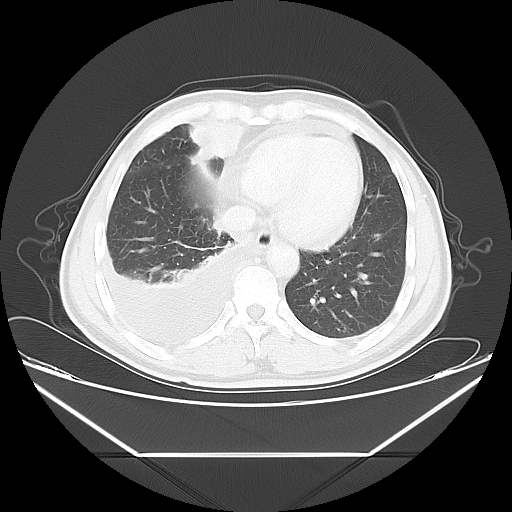
Chest CT, one axial slice; slice 15 of 56 in the series (ordered by position); reconstruction kernel LUNG; 120 kVp; lung window (W 1500 / L -600 HU); 5 mm slice thickness; 512 × 512 image matrix, field of view 412 × 412 mm. Male patient, age 57 years. From the clinical record (not read from this slice): clinical TNM (as recorded): T2 N3 M1.
Outlined on this slice (bounding box drawn by a radiologist):
- lung tumour (recorded histology: adenocarcinoma): bounding box <178,114,246,162> (left, top, right, bottom; pixels)